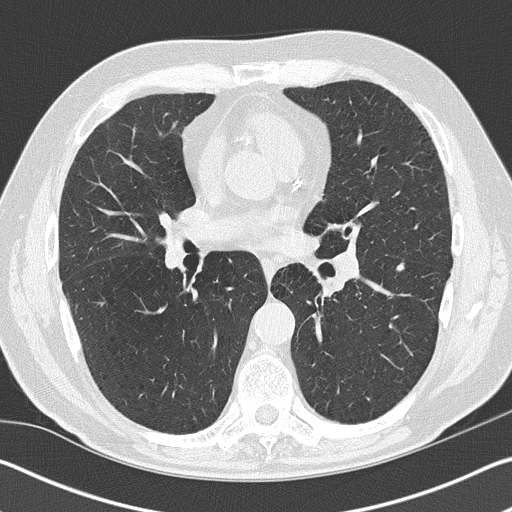
Axial slice from a low-dose chest CT screening exam; baseline annual screen; lung window (W 1500 / L -600 HU); 2 mm slice thickness; slice 81 of 161 in the series; 512 × 512 image matrix. Male, age 65 years at enrolment. Current smoker at enrolment.
• Expert reader's lesion annotation, bounding box [x1, y1, x2, y2] px = [383, 253, 420, 285].
• Screening reader's record for this exam: no non-calcified nodule ≥4 mm recorded.
• Official screen result: negative screen, minor abnormalities not suspicious for lung cancer.
• Later outcome: lung cancer diagnosed 460 days after this screen — non-small cell carcinoma, left lower lobe, right hilum, poorly differentiated (G3), stage IV (AJCC 6th edition), 5 mm at pathology.